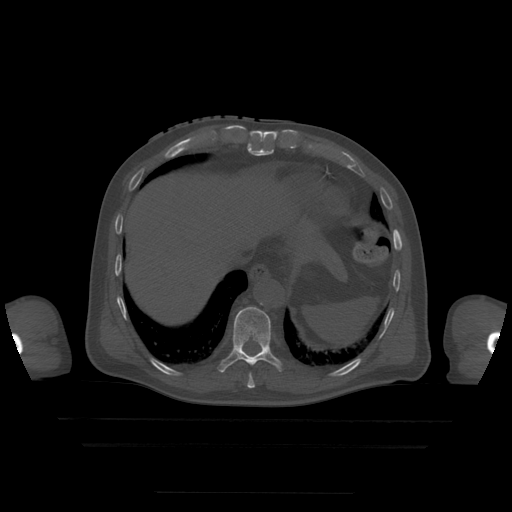
CT including the spine, one axial slice. Bone window (W 1800 / L 400 HU). 1.25 mm slice thickness. 512 × 512 image matrix, field of view 436 × 436 mm. Patient age 68 years. From the clinical record (not read from this slice): primary cancer: urothelial.
Annotated regions visible in this slice (semi-automatic segmentation, software-assisted and operator-edited):
- T10 vertebra: box from (x=219, y=307) to (x=283, y=373) px
- T9 vertebra: (x=247, y=374)–(x=255, y=389)